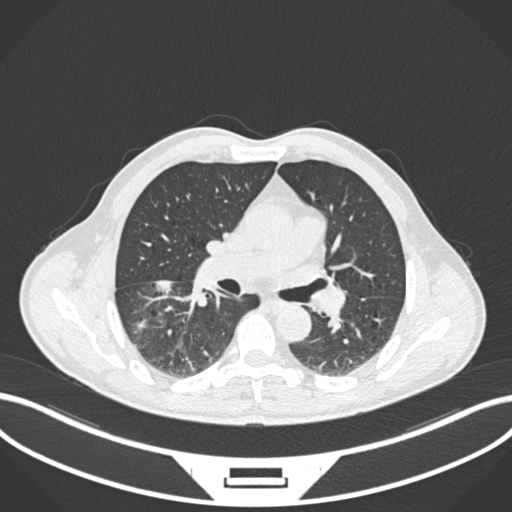
Chest CT, one axial slice; slice 112 of 208 in the series (ordered by position); 120 kVp; lung window (W 1500 / L -600 HU); 512 × 512 image matrix. Patient: male, 58 years. Case-level facts recorded for this patient, not image findings: clinical TNM (as recorded): T3 N0 M0.
Structures marked on this image (bounding box drawn by a radiologist):
- lung tumour (recorded histology: squamous cell carcinoma): box from (x=151, y=273) to (x=176, y=296) px